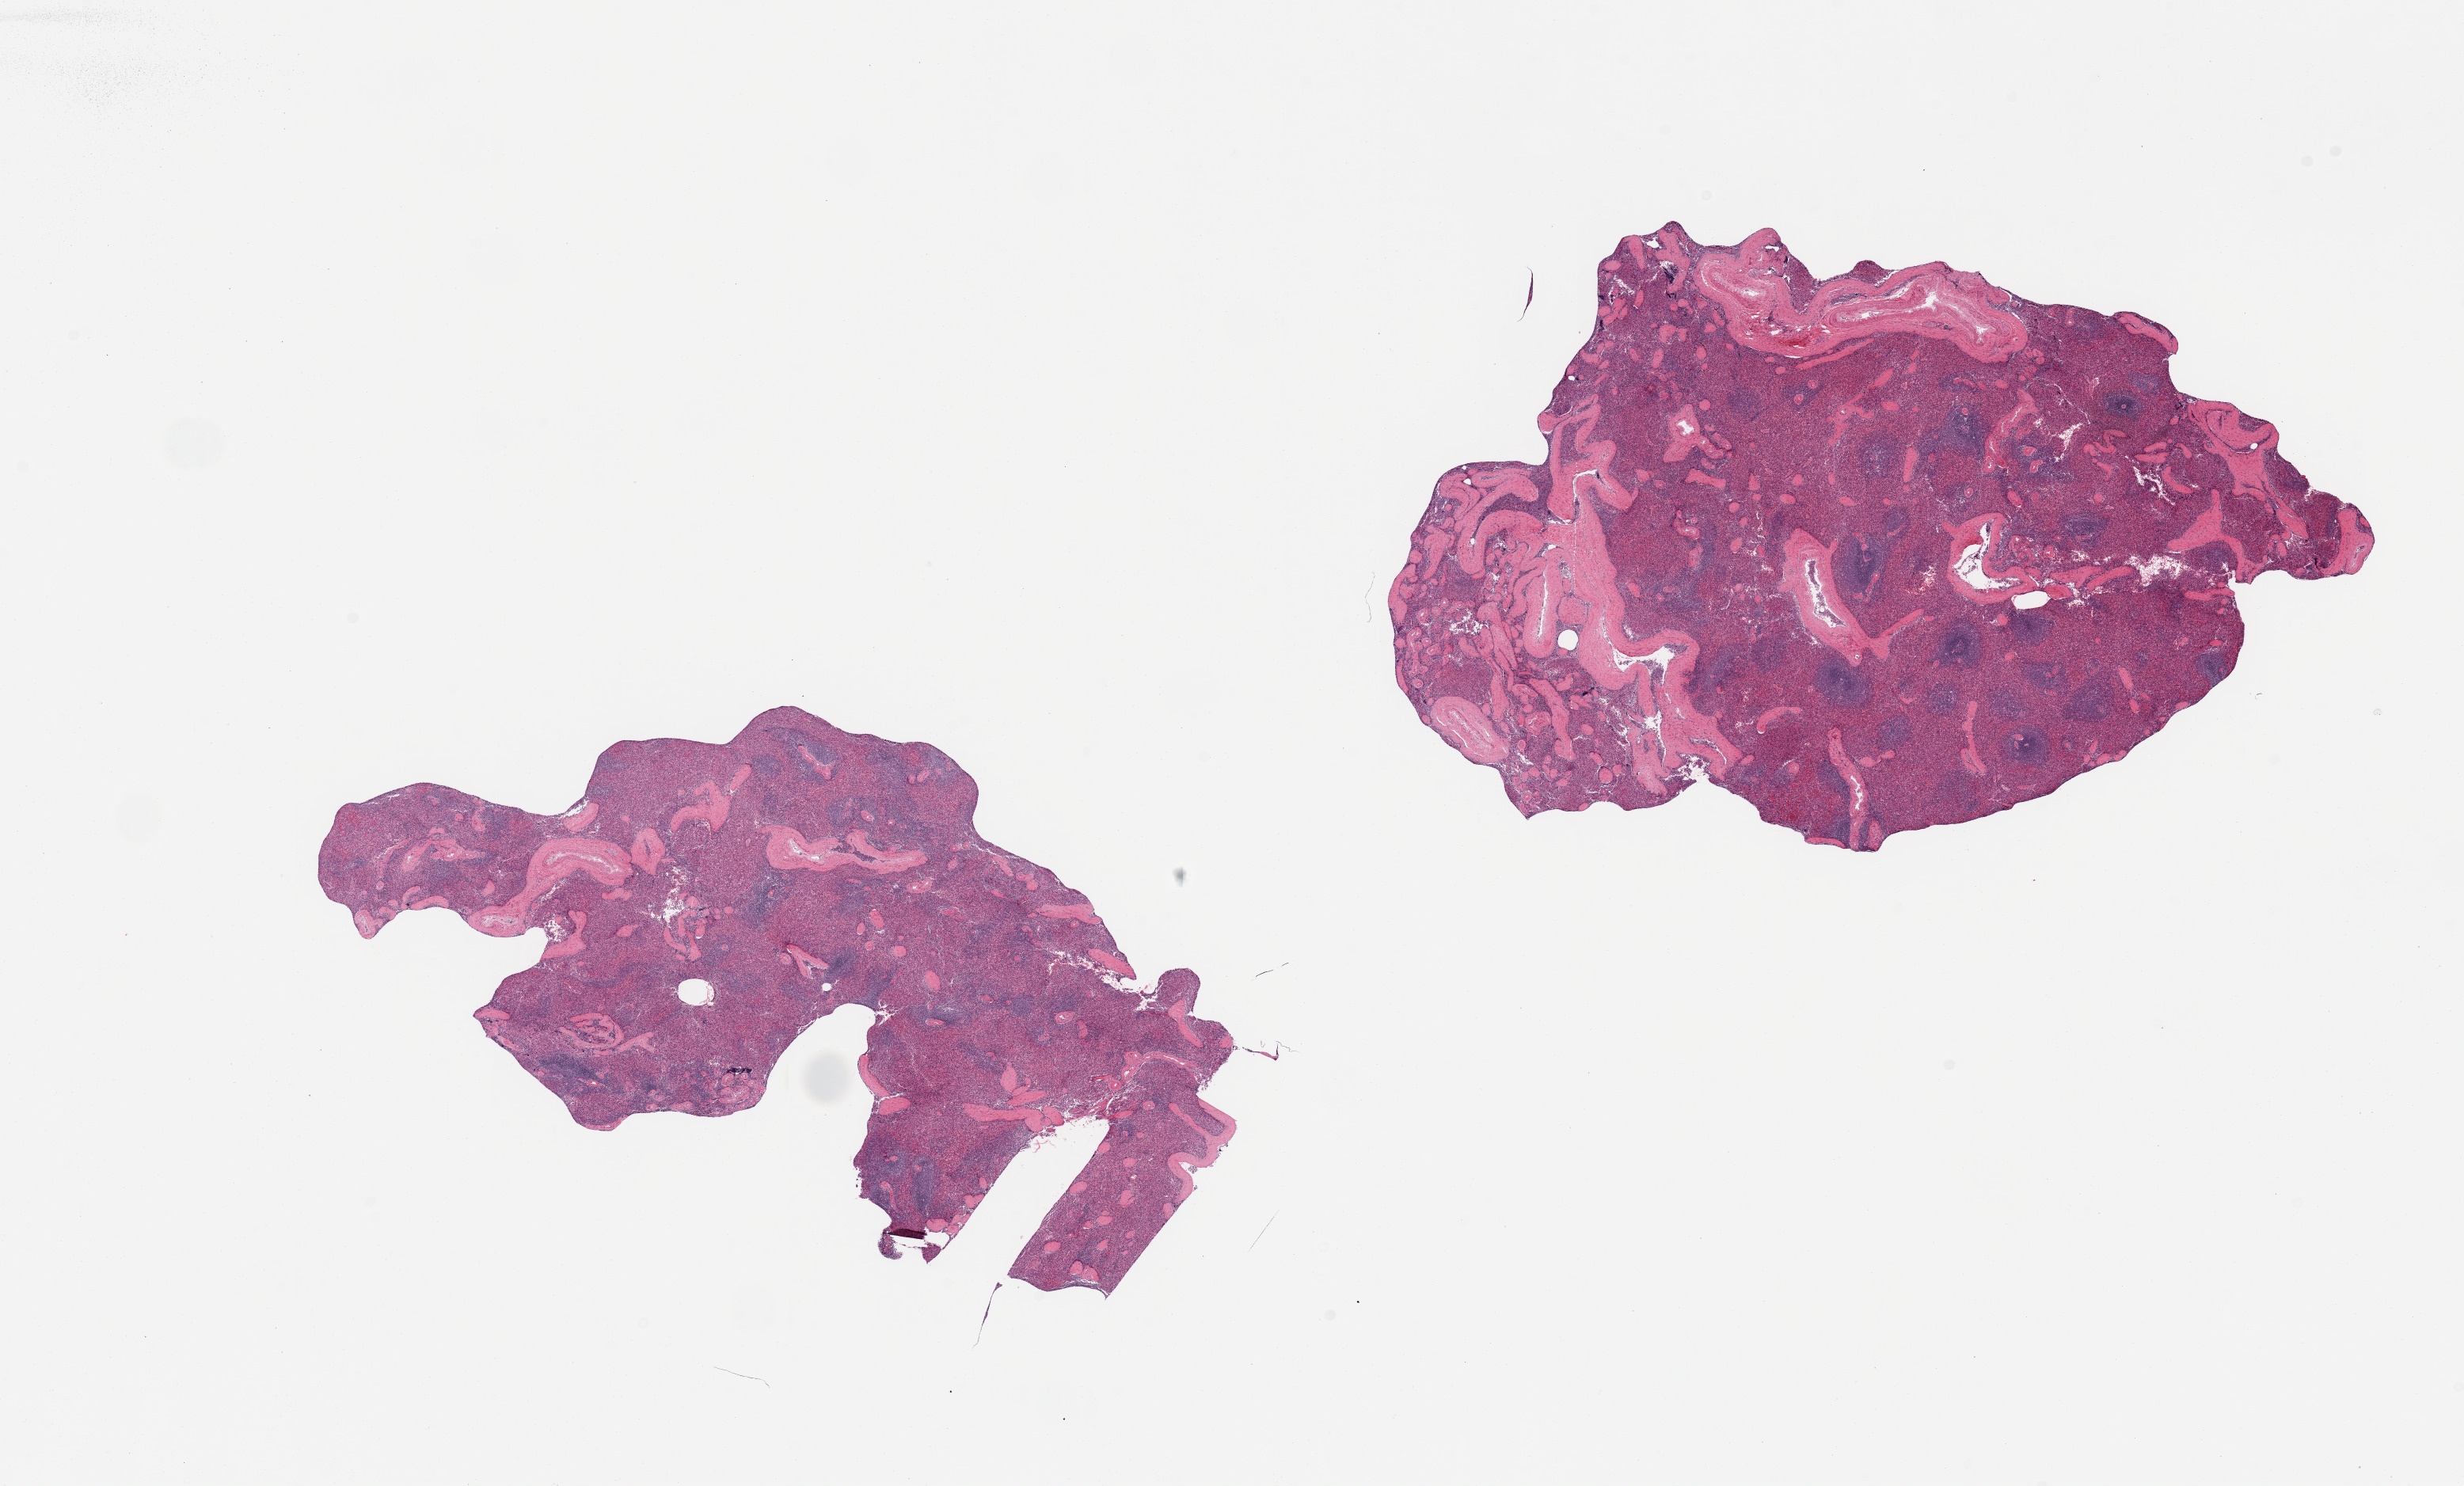
H&E whole-slide image, brightfield — whole scanned area (about 24.6 x 14.8 mm) shown as a low-resolution overview. PAXgene-fixed, paraffin-embedded tissue. Sampled site (target tissue): spleen. Donor tissue sample. Donor: female.
Review note (as recorded): 2 pieces; numerous blood vessels focally.